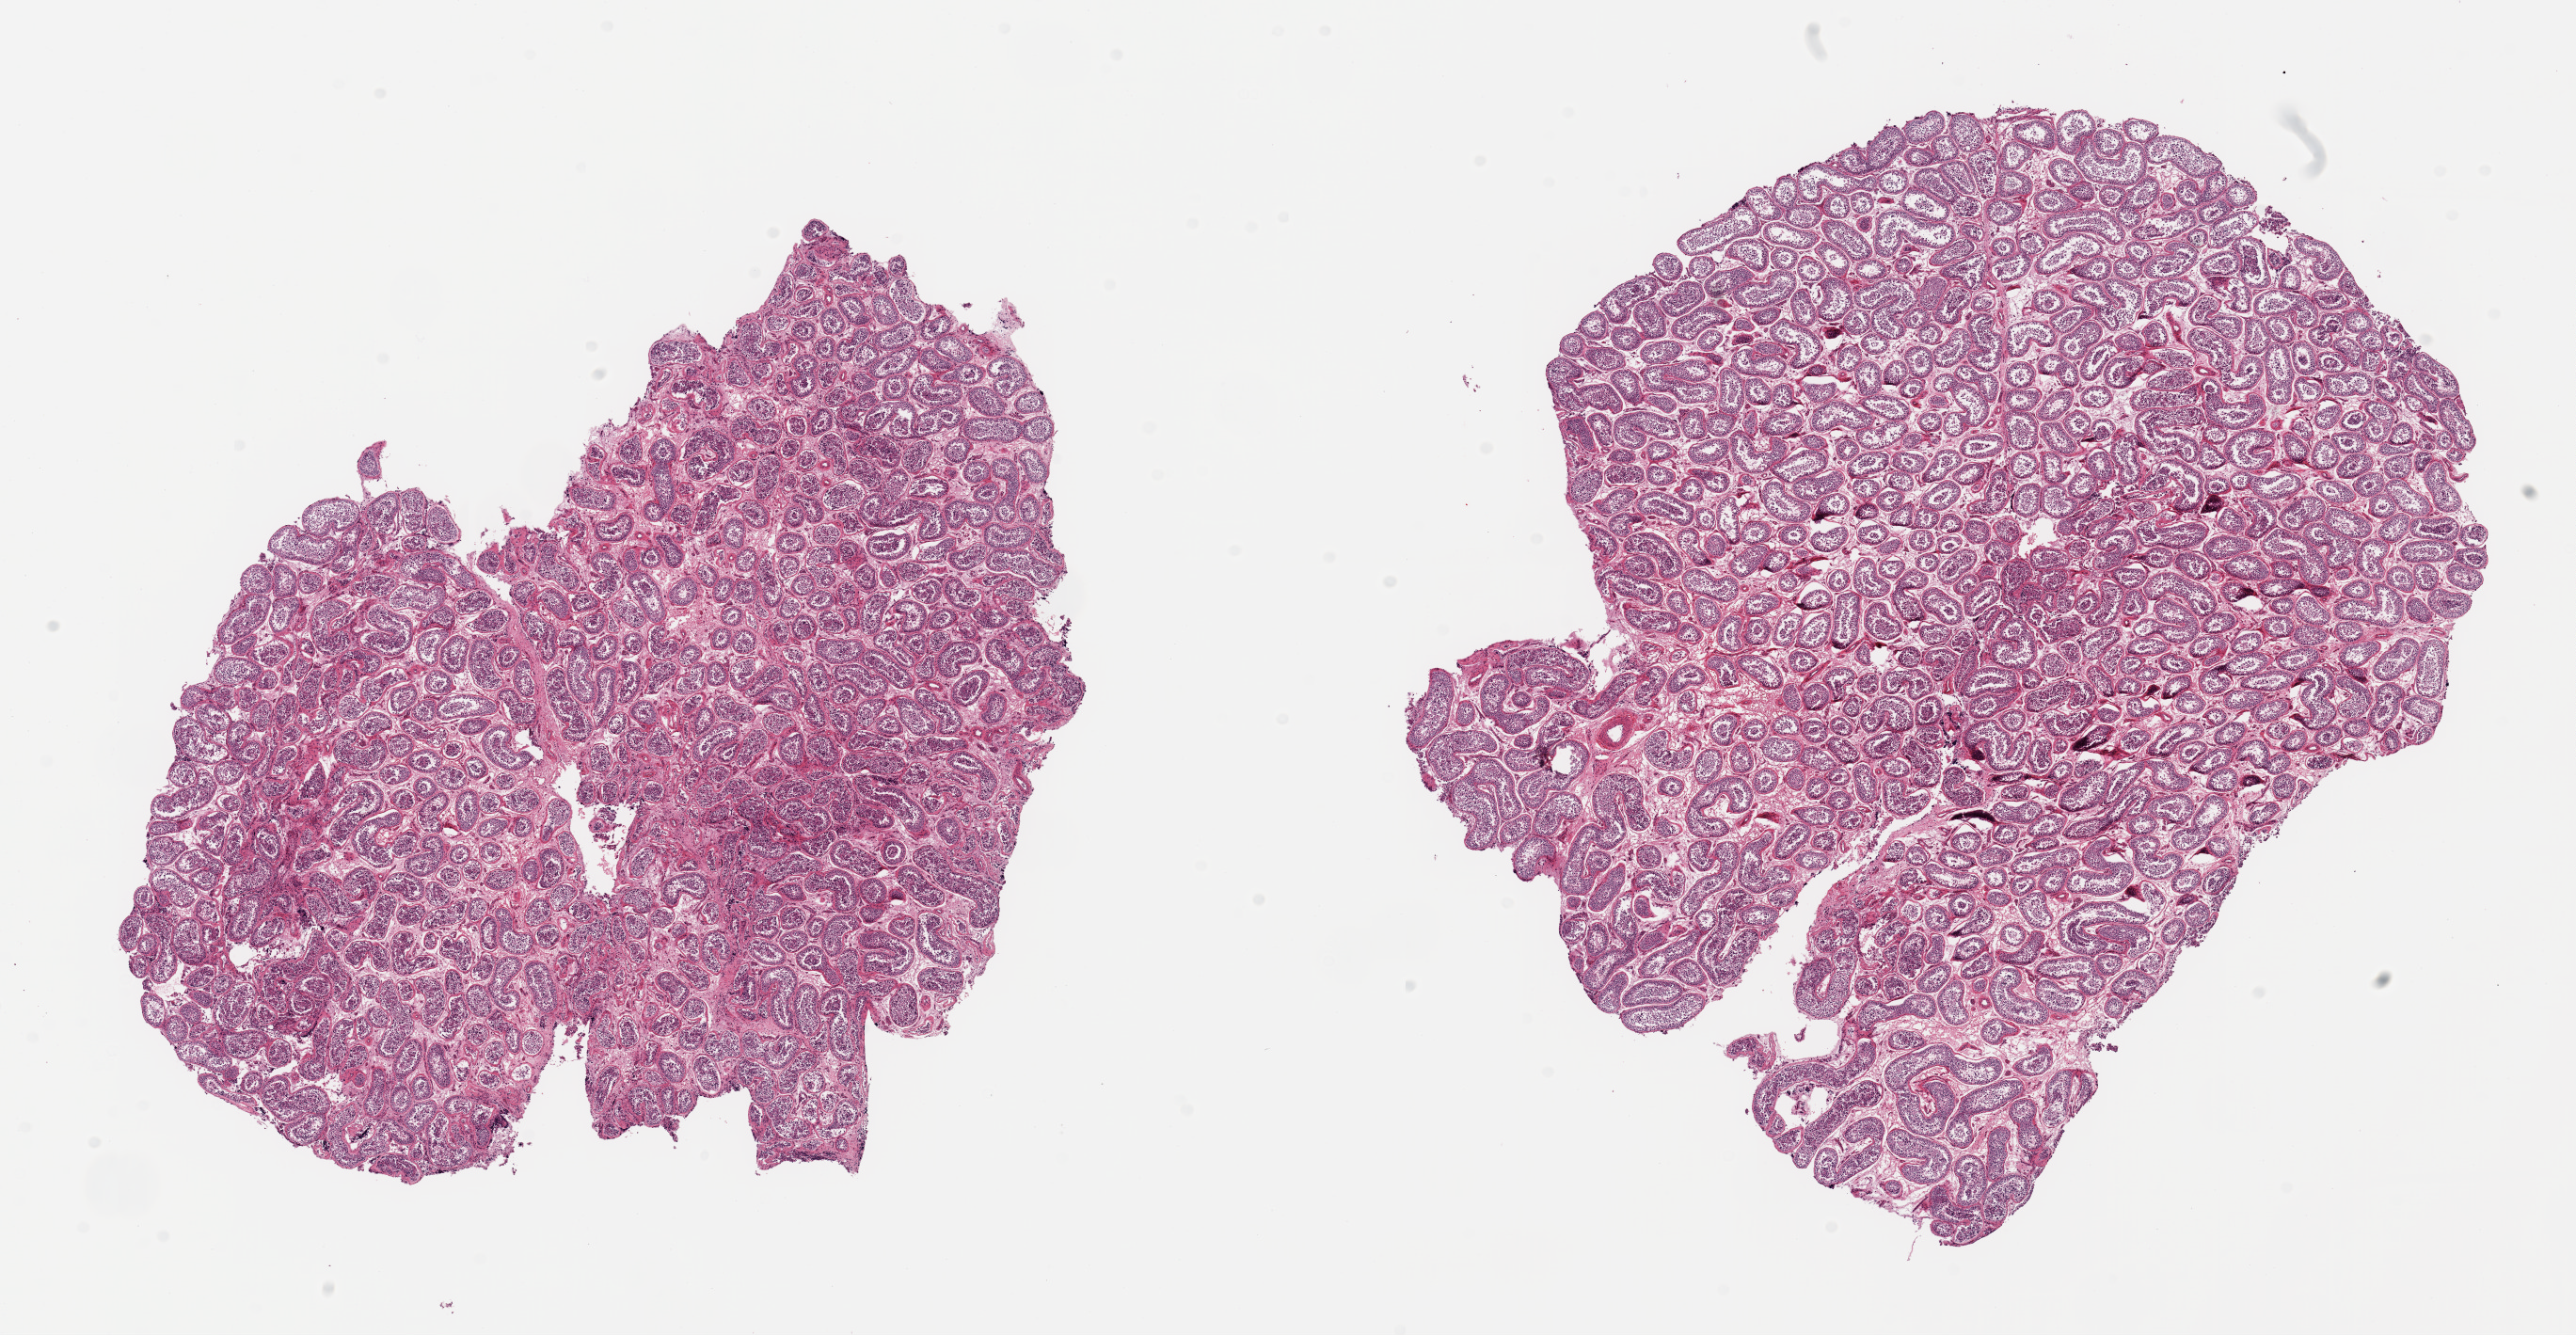
Hematoxylin and eosin (H&E) whole-slide image, brightfield — low-resolution overview of the scanned area, about 21.7 x 11.2 mm (acquisition: 20x scan), PAXgene-fixed, paraffin-embedded tissue, section of testis (target tissue), tissue donor sample. Donor sex: male.
Pathologist's review note for this sample: 2 pieces, spermatogenesis is present.